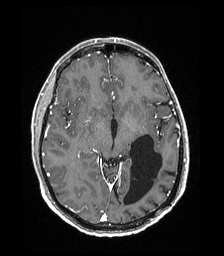
Brain MRI from a brain-tumour surgery series, one axial slice. Position 102 of 192 along the scan axis. T1-weighted post-contrast. 224 × 256 image matrix. From the clinical record (not read from this slice): histopathology: Low grade glioma; IDH mutation: no; tumour location: Left Parieto-Occipital Intraventricular.
Structures marked on this image (outlined manually by an expert reader):
- previous resection cavity: bounding box [x1, y1, x2, y2] px = [124, 135, 162, 205]